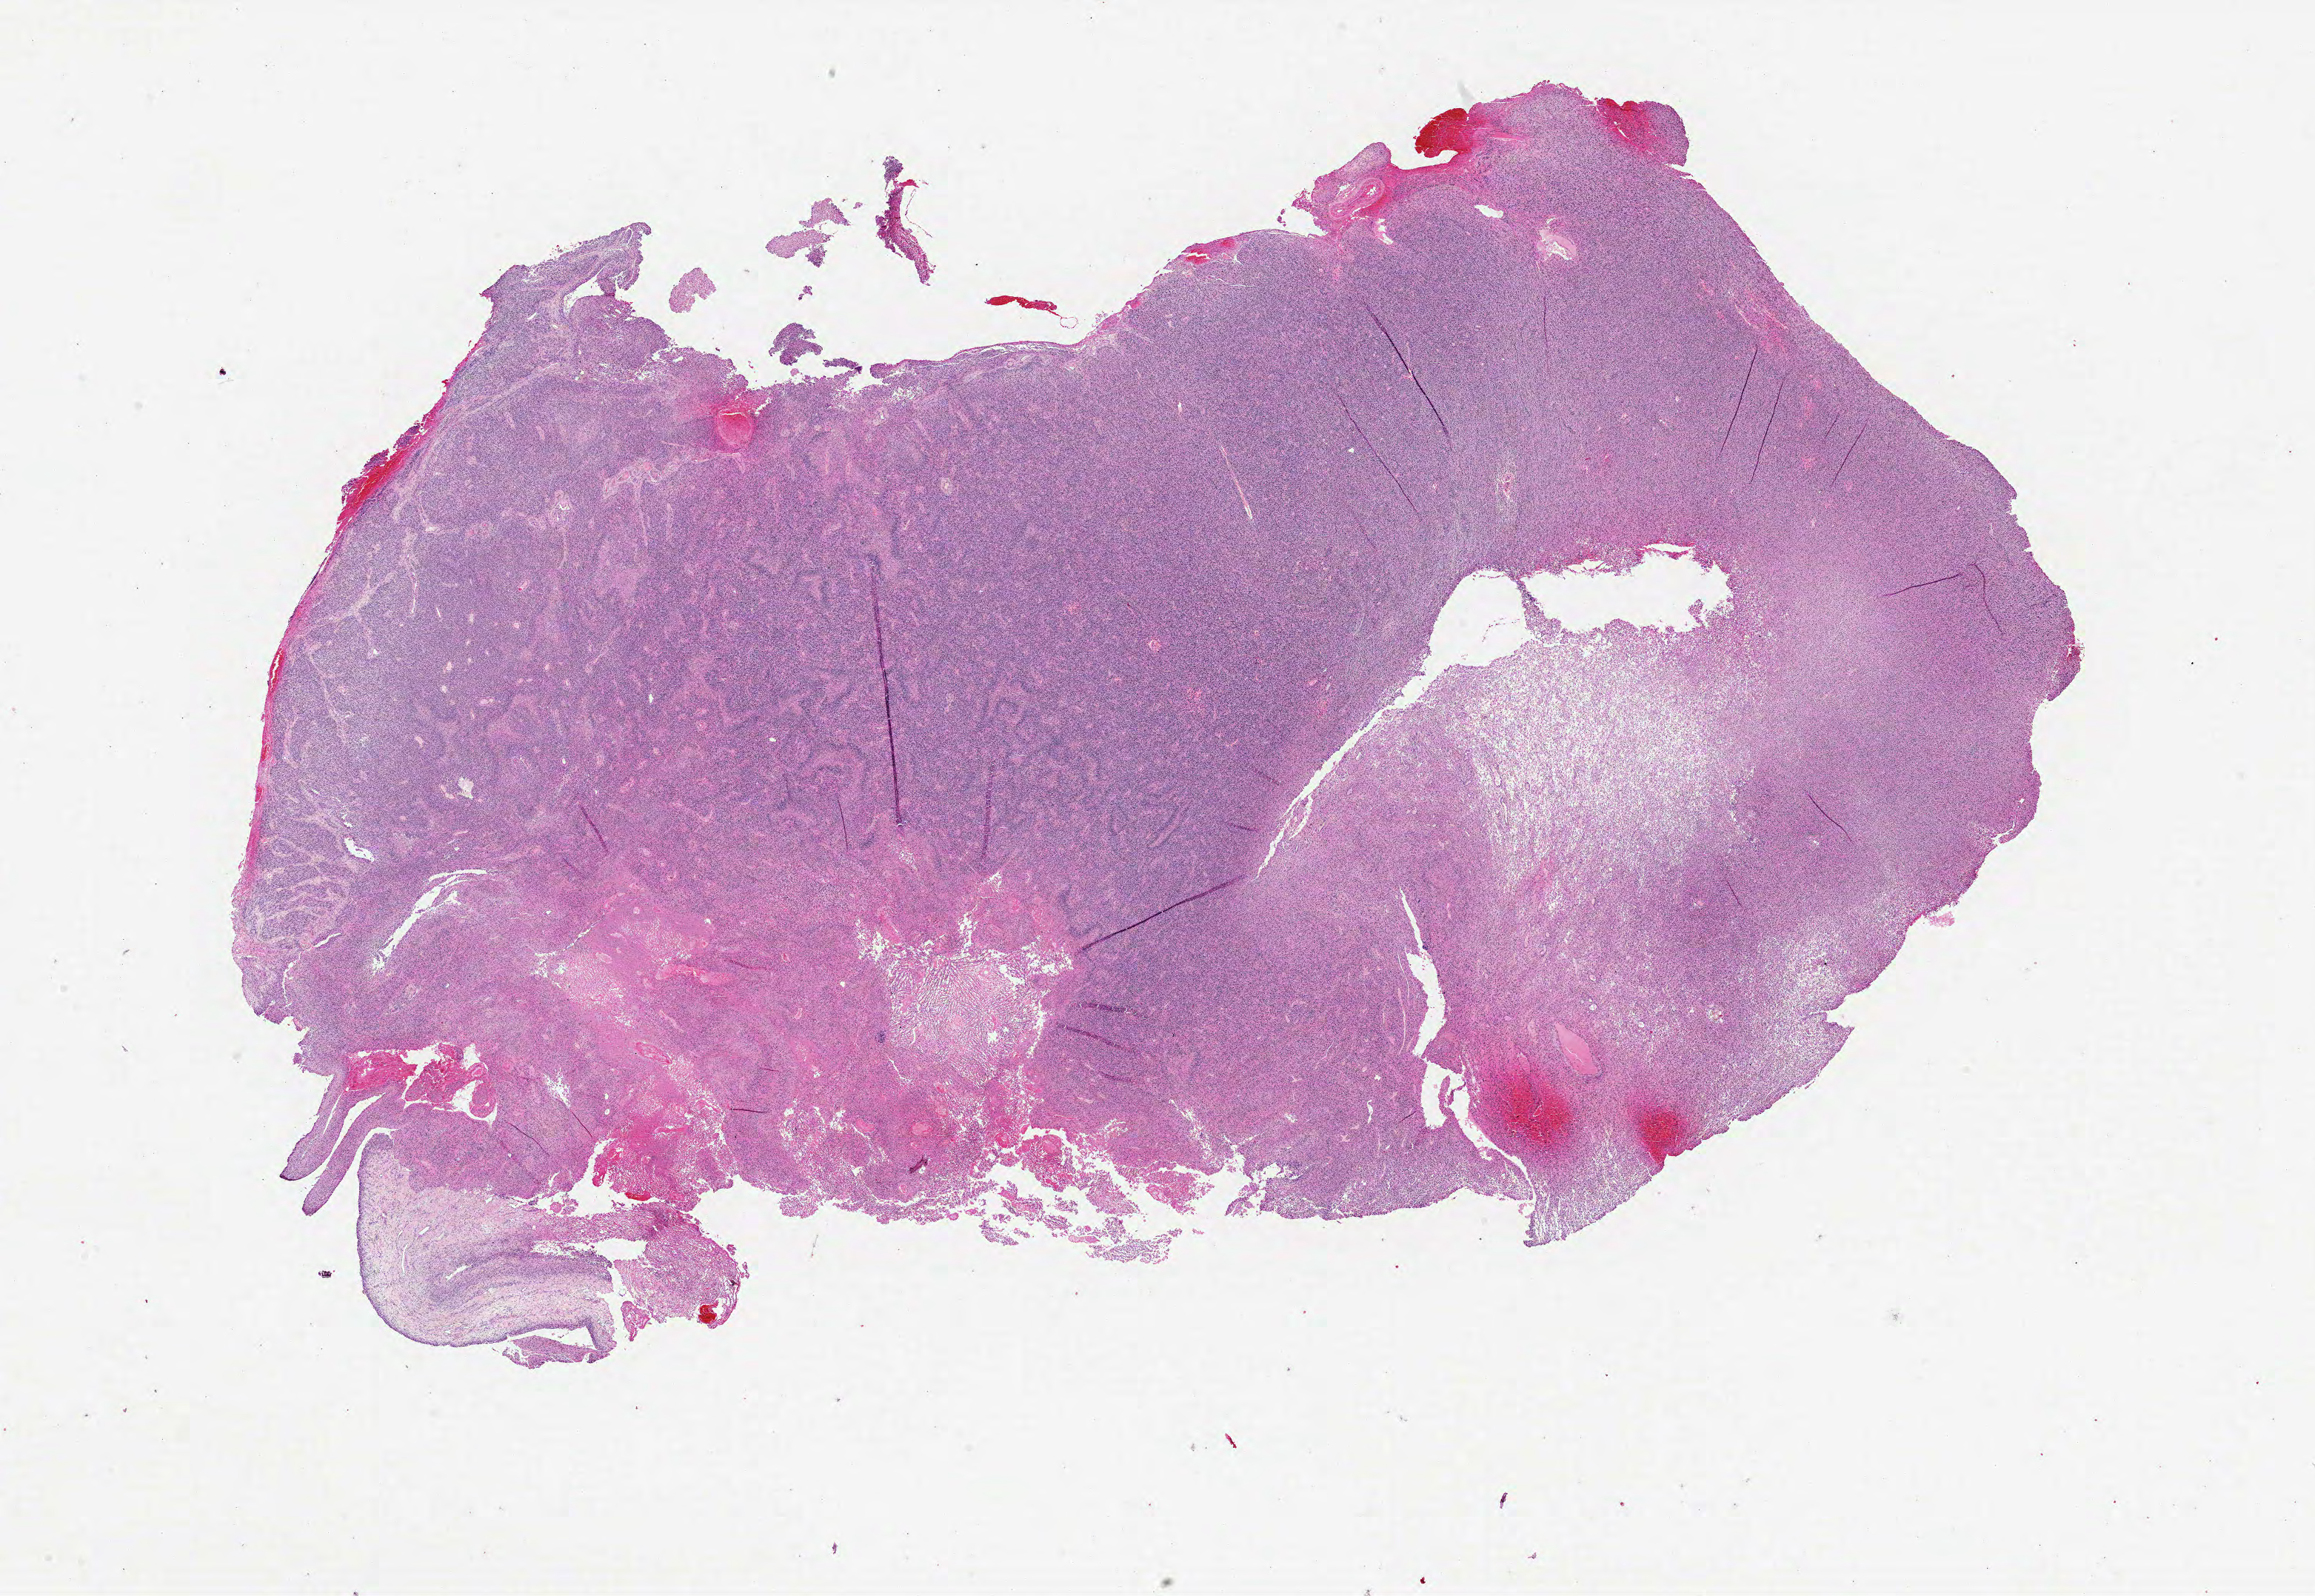
Digitized H&E-stained tissue section (whole slide) — low-resolution overview of the scanned area, about 25.0 x 17.2 mm (acquisition: 20x scan). Formalin-fixed paraffin-embedded (FFPE) diagnostic section. Sample: primary tumour, brain. Female, age 10 years at initial diagnosis.
Diagnosis: Glioblastoma.